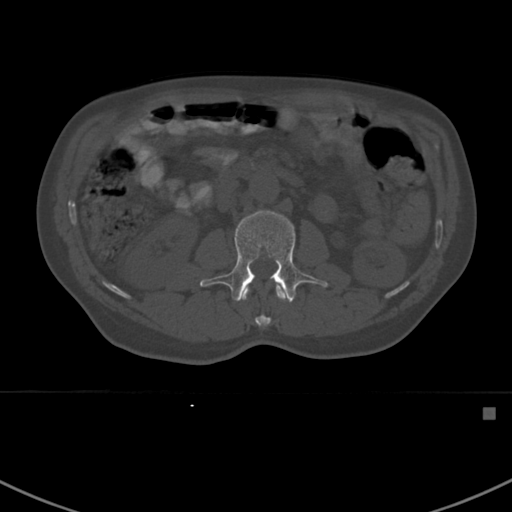
CT including the spine, one axial slice. Slice 290 of 412 in the series (ordered by position). Reconstruction kernel Br40s. Bone window (W 1800 / L 400 HU). 1.5 mm slice thickness. 512 × 512 image matrix, field of view 358 × 358 mm. Male patient, age 59 years. Case-level facts recorded for this patient, not image findings: primary cancer: prostate.
Structures marked on this image (semi-automatic segmentation, software-assisted and operator-edited):
- L1 vertebra: bounding box <242,286,286,328> (left, top, right, bottom; pixels)
- L2 vertebra: <200,209,328,302>